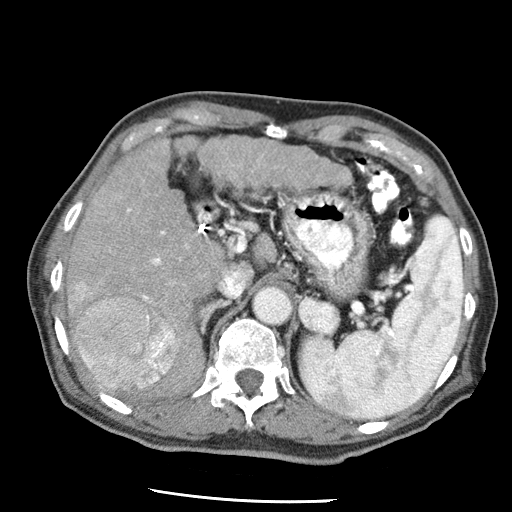
Contrast-enhanced abdominal CT (liver protocol), one axial slice; slice 34 of 79 in the series (ordered by position); soft-tissue window (W 400 / L 40 HU); 2.5 mm slice thickness; 512 × 512 image matrix, field of view 320 × 320 mm. Case-level facts recorded for this patient, not image findings: diagnosis: hepatocellular carcinoma (patient treated with transarterial chemoembolisation; whether this scan precedes or follows treatment is not stated here); TNM stage (as recorded): Stage-IIIA; Child-Pugh class: A; tumour nodularity: multinodular.
Annotated regions visible in this slice (semi-automatically segmented with operator editing):
- liver parenchyma outside the tumour (the mass and vessels are separate outlines, so this box may not span the whole liver): box from (x=66, y=136) to (x=352, y=398) px
- mass: (x=68, y=281)–(x=179, y=393)
- liver vessels: (x=127, y=208)–(x=207, y=381)